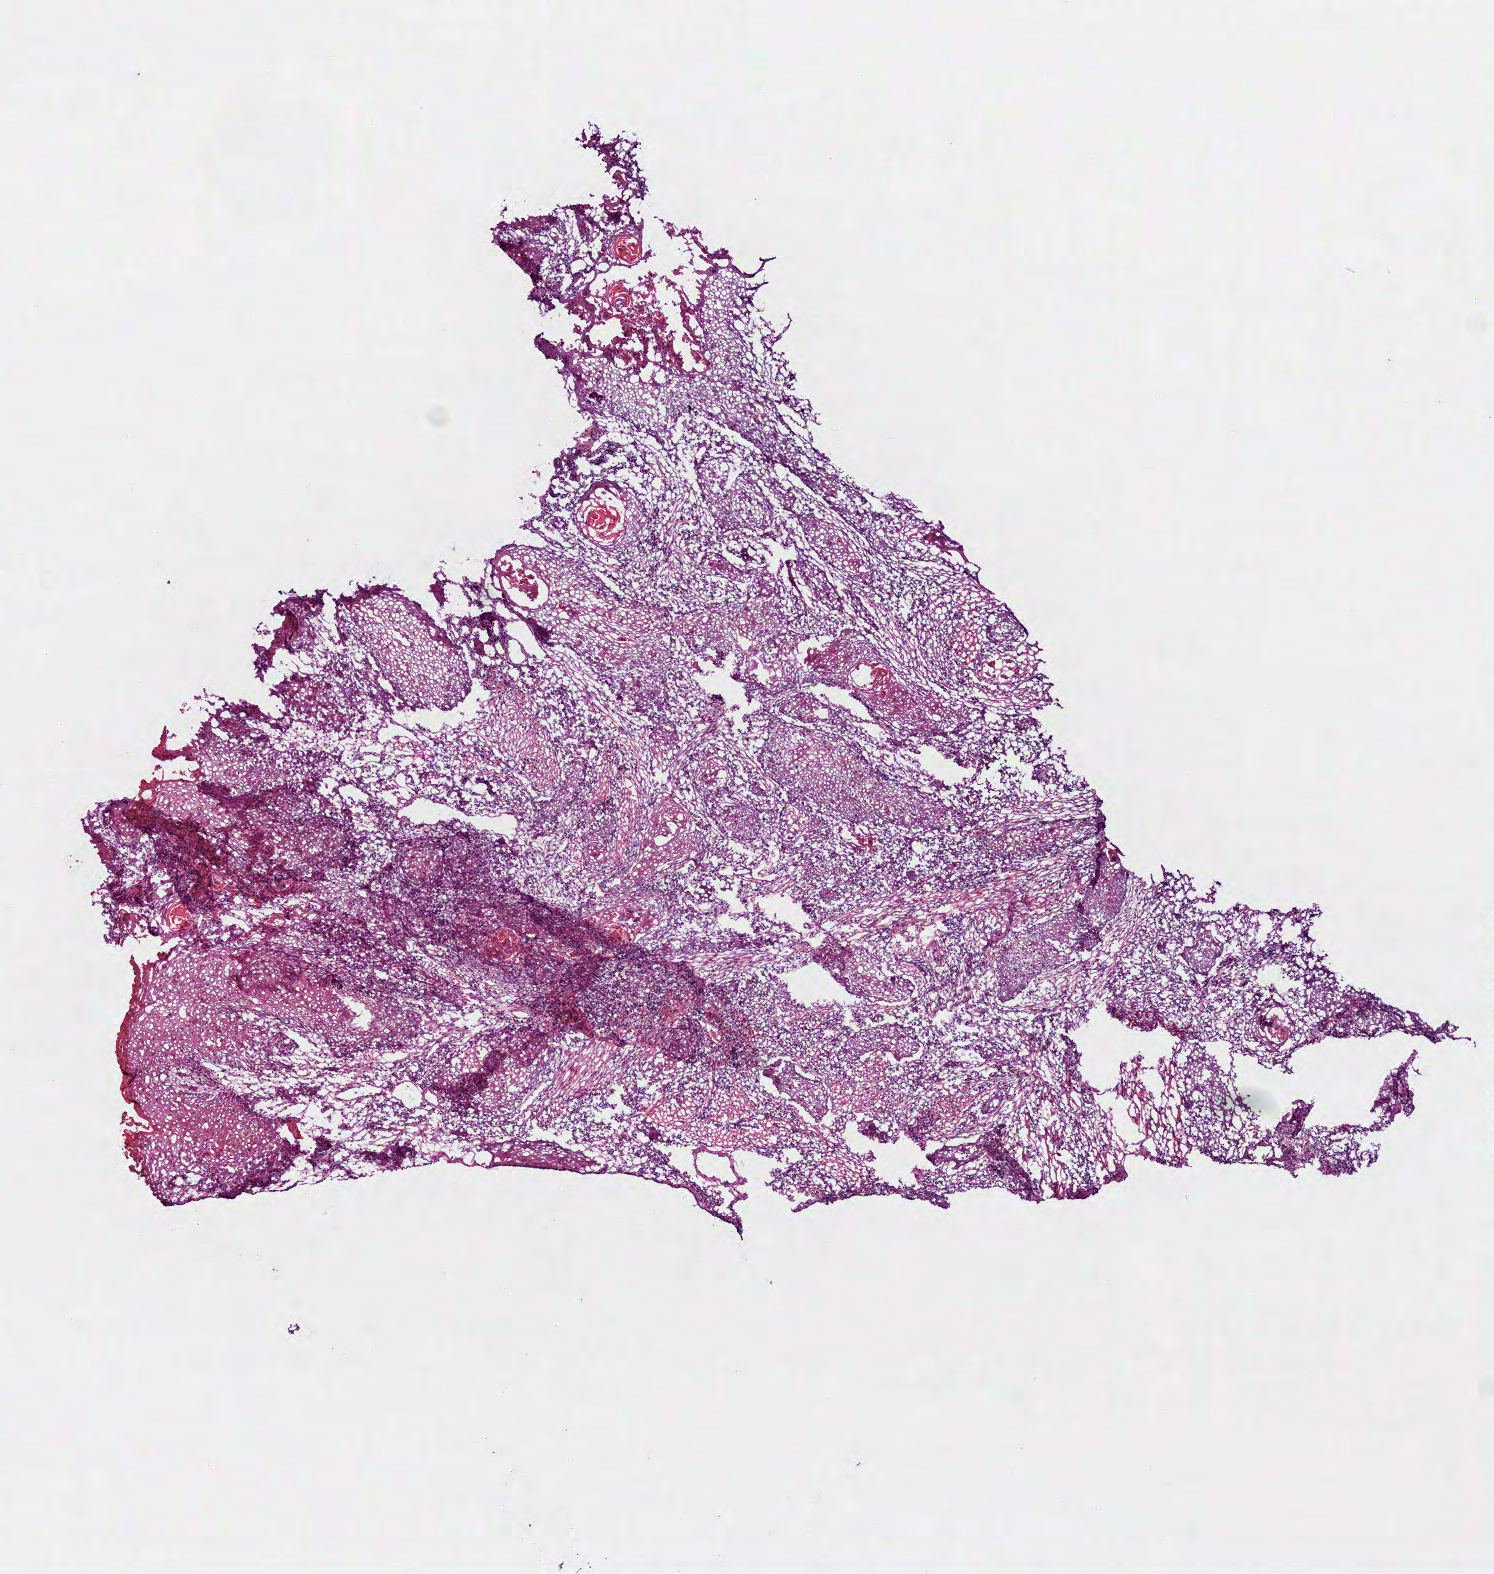
Digitized H&E-stained tissue section (whole slide), low-resolution overview of the scanned area, about 6.0 x 6.3 mm (from a 40x scan). Frozen section from the top of the tissue portion. Head and neck, primary tumour sample. Male, age 63 years at initial diagnosis. Histologic grade: G2 (moderately differentiated). Composition of this section per pathologist review: tumour cells 90%, tumour nuclei 85%, normal cells 0%, stromal cells 10%, necrosis 0%.
* diagnosis: Squamous cell carcinoma, NOS (tongue, NOS)
* laterality: right
* AJCC pathologic stage: IVA (6th edition)